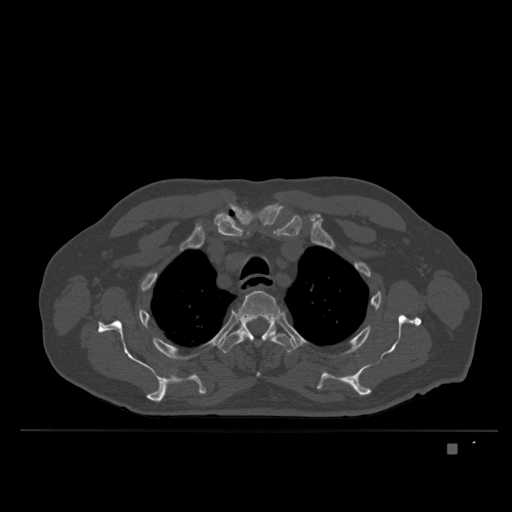
CT including the spine, one axial slice; slice 294 of 435 in the series (ordered by position); bone window (W 1800 / L 400 HU); 1.5 mm slice thickness; 512 × 512 image matrix, field of view 434 × 434 mm. Patient: male, 73 years. From the clinical record (not read from this slice): primary cancer: skin.
Structures marked on this image (semi-automatically segmented with operator editing):
- T3 vertebra: box from (x=237, y=290) to (x=281, y=377) px
- T4 vertebra: (x=218, y=320)–(x=297, y=354)